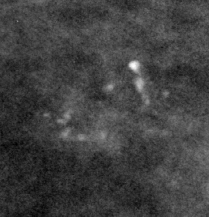
Region of interest cut from a scanned film mammogram (one marked finding); right breast; CC view; BI-RADS breast density category 2 (scale 1–4).
Finding: calcifications, morphology pleomorphic, distribution clustered; BI-RADS assessment category 4; subtlety rating 3 on a 1 (subtle) to 5 (obvious) scale; pathology result (as recorded, not read from the image): malignant.